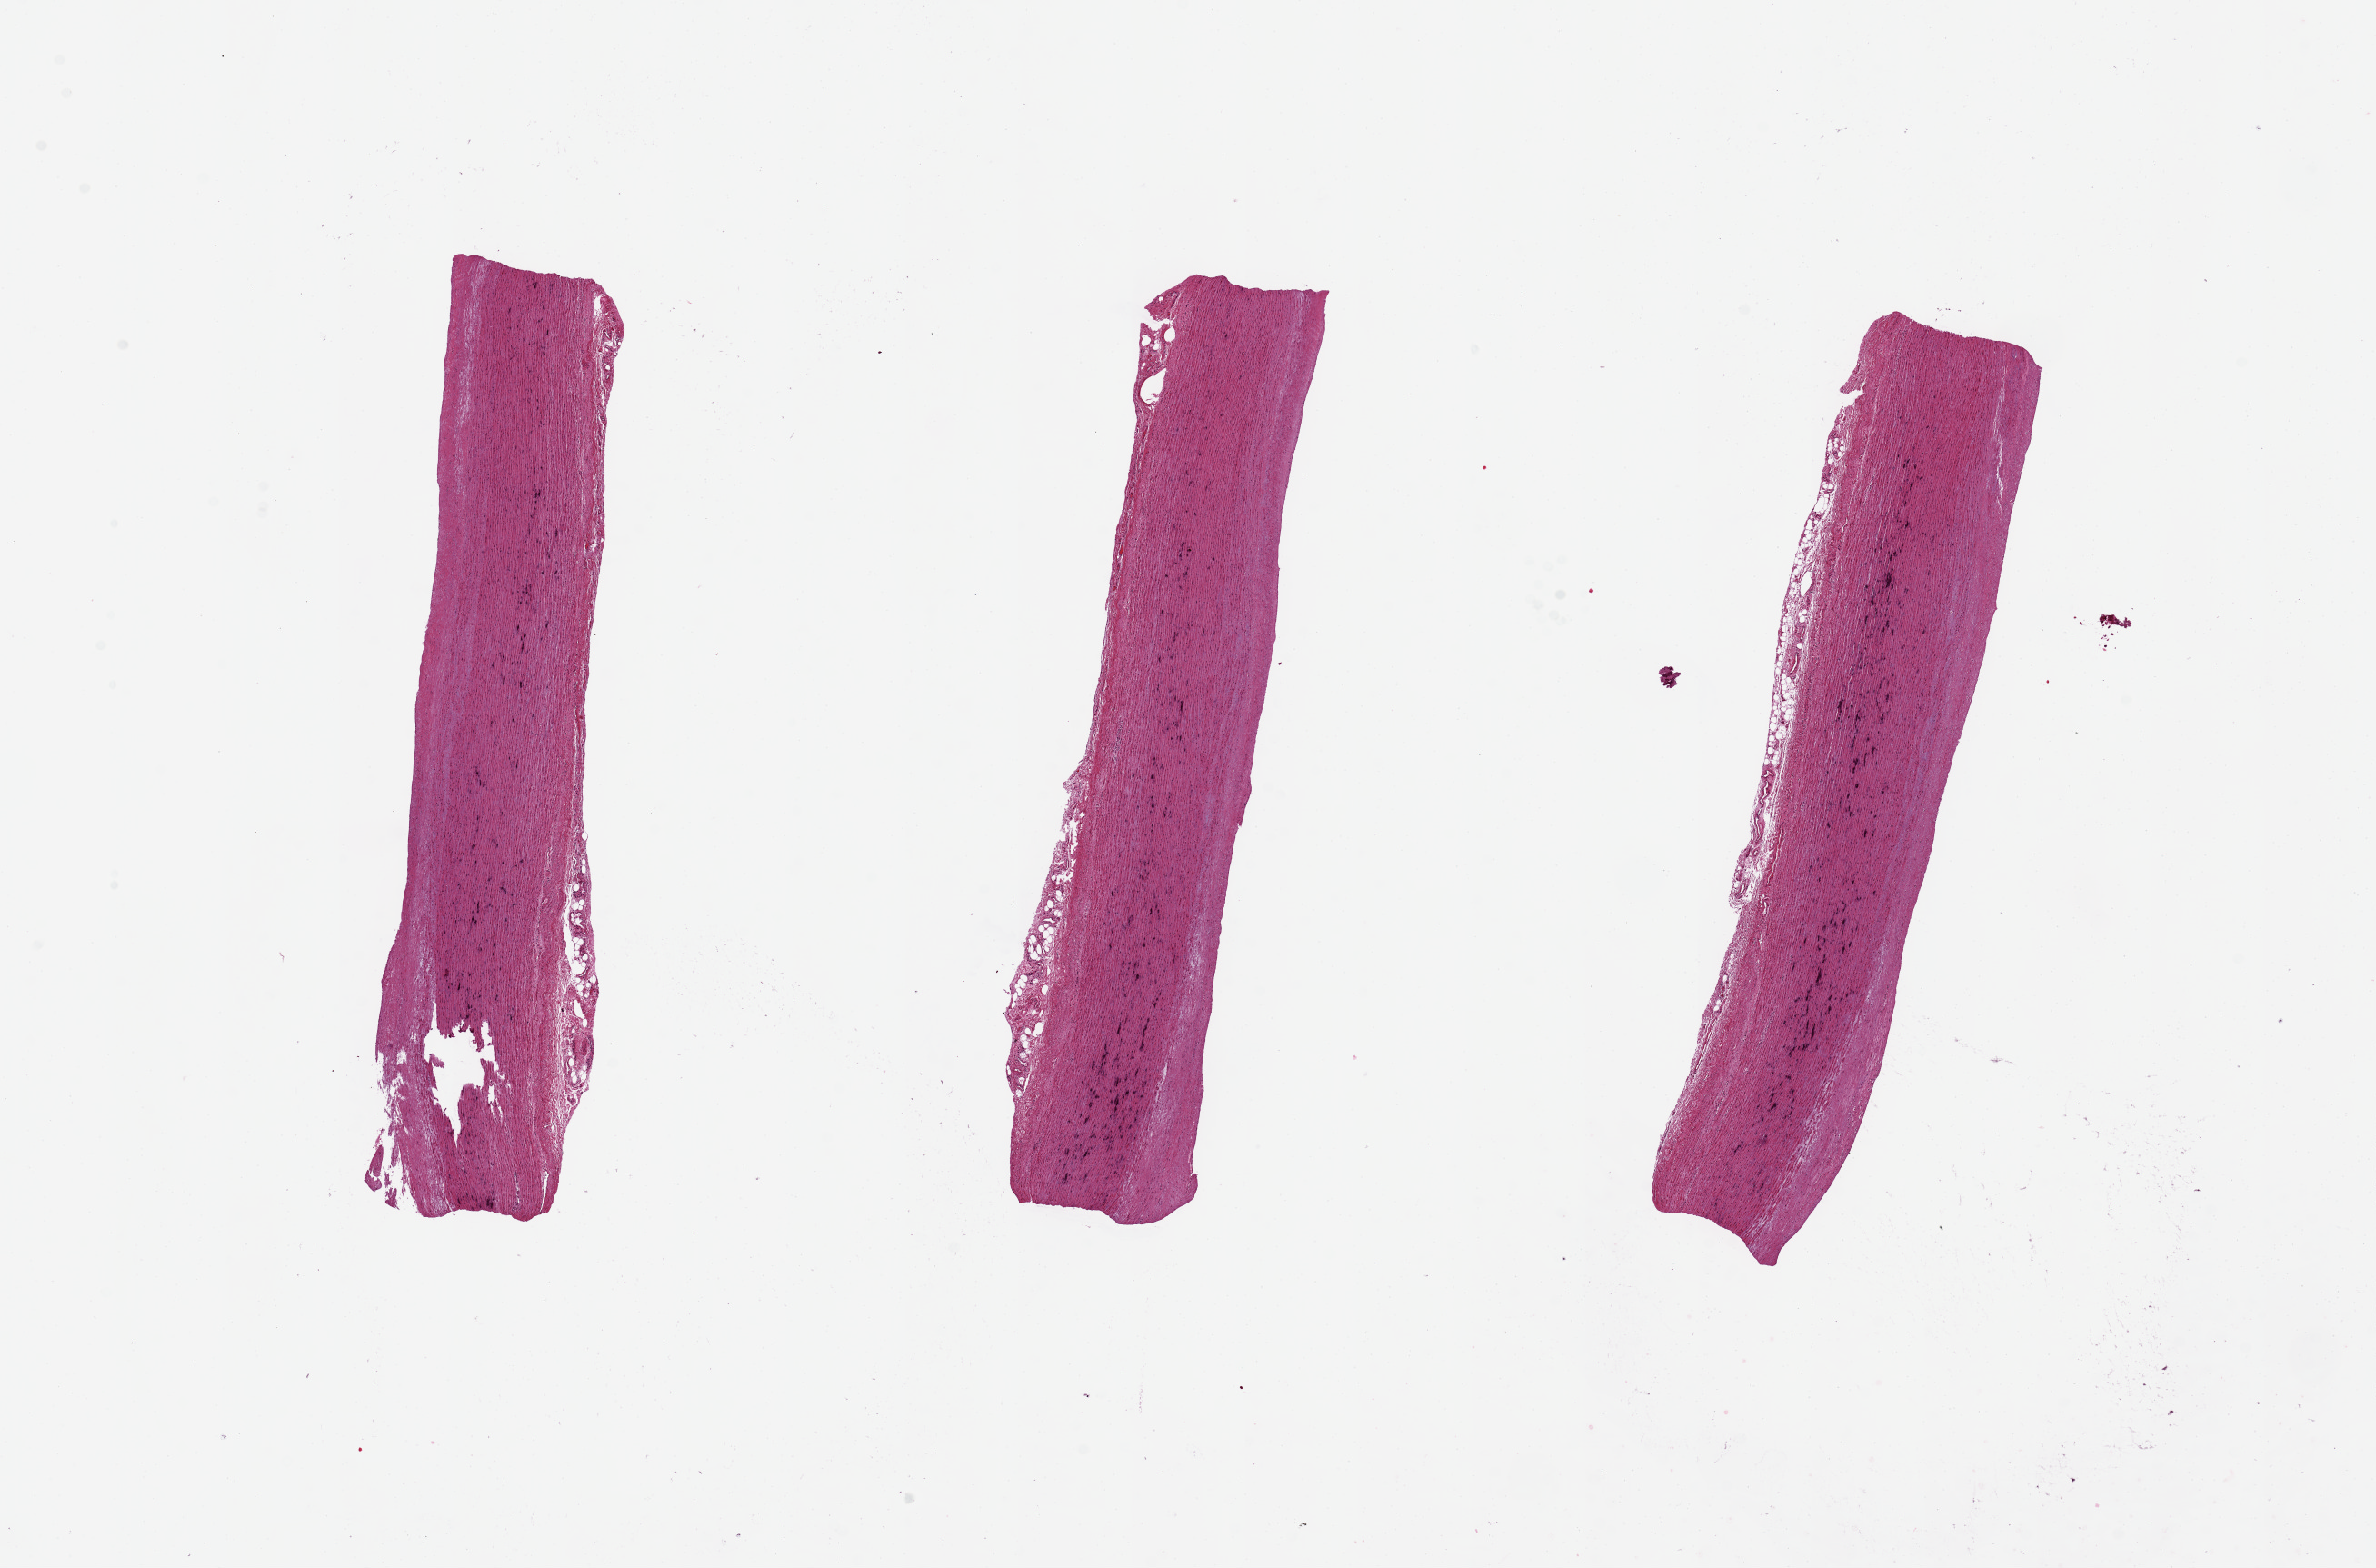
H&E whole-slide image, brightfield, whole scanned area (about 20.7 x 13.6 mm) shown as a low-resolution overview; PAXgene-fixed paraffin-embedded (PFPE) section; sampled site (target tissue): aorta; donor tissue sample. Donor sex: female.
• reviewer comment on this tissue sample: 3 pieces 8x1.5 mm; punctate medial calcification